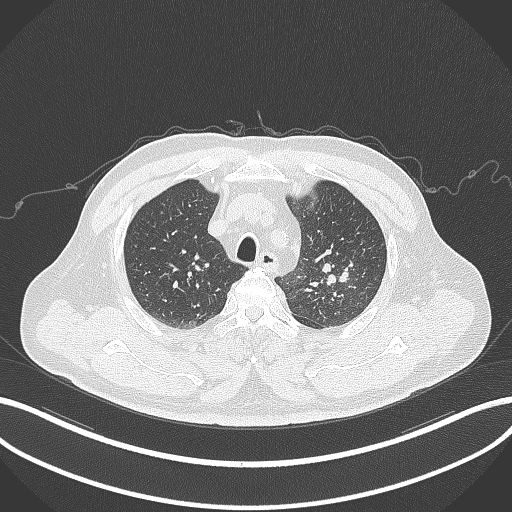
Chest CT, one axial slice; position 243 of 286 along the scan axis; reconstruction kernel B70f; 120 kVp; lung window (W 1500 / L -600 HU); 1 mm slice thickness; 512 × 512 image matrix, field of view 400 × 400 mm. Patient: male, 67 years. From the clinical record (not read from this slice): clinical TNM (as recorded): T2a N1 M0; histopathological grade: G3.
Outlined on this slice (bounding box drawn by a radiologist):
- lung tumour (recorded histology: adenocarcinoma): bounding box <318,257,352,289> (left, top, right, bottom; pixels)